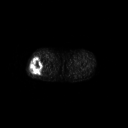
FDG PET of an extremity soft-tissue mass (from a PET/CT study), one axial slice; slice 250 of 267 in the series (ordered by position); 3.27 mm slice thickness; 128 × 128 image matrix, field of view 700 × 700 mm. Male patient, age 43 years. Case-level facts recorded for this patient, not image findings: histological type: poorly differentiated synovial sarcoma; grade: high; site of the primary tumour: right buttock.
Annotated regions visible in this slice (expert contour drawn on MRI and transferred to this co-registered scan by the dataset authors):
- gross tumour volume including surrounding oedema: bounding box [x1, y1, x2, y2] px = [29, 57, 45, 75]
- gross tumour volume (mass): [29, 57, 44, 75]